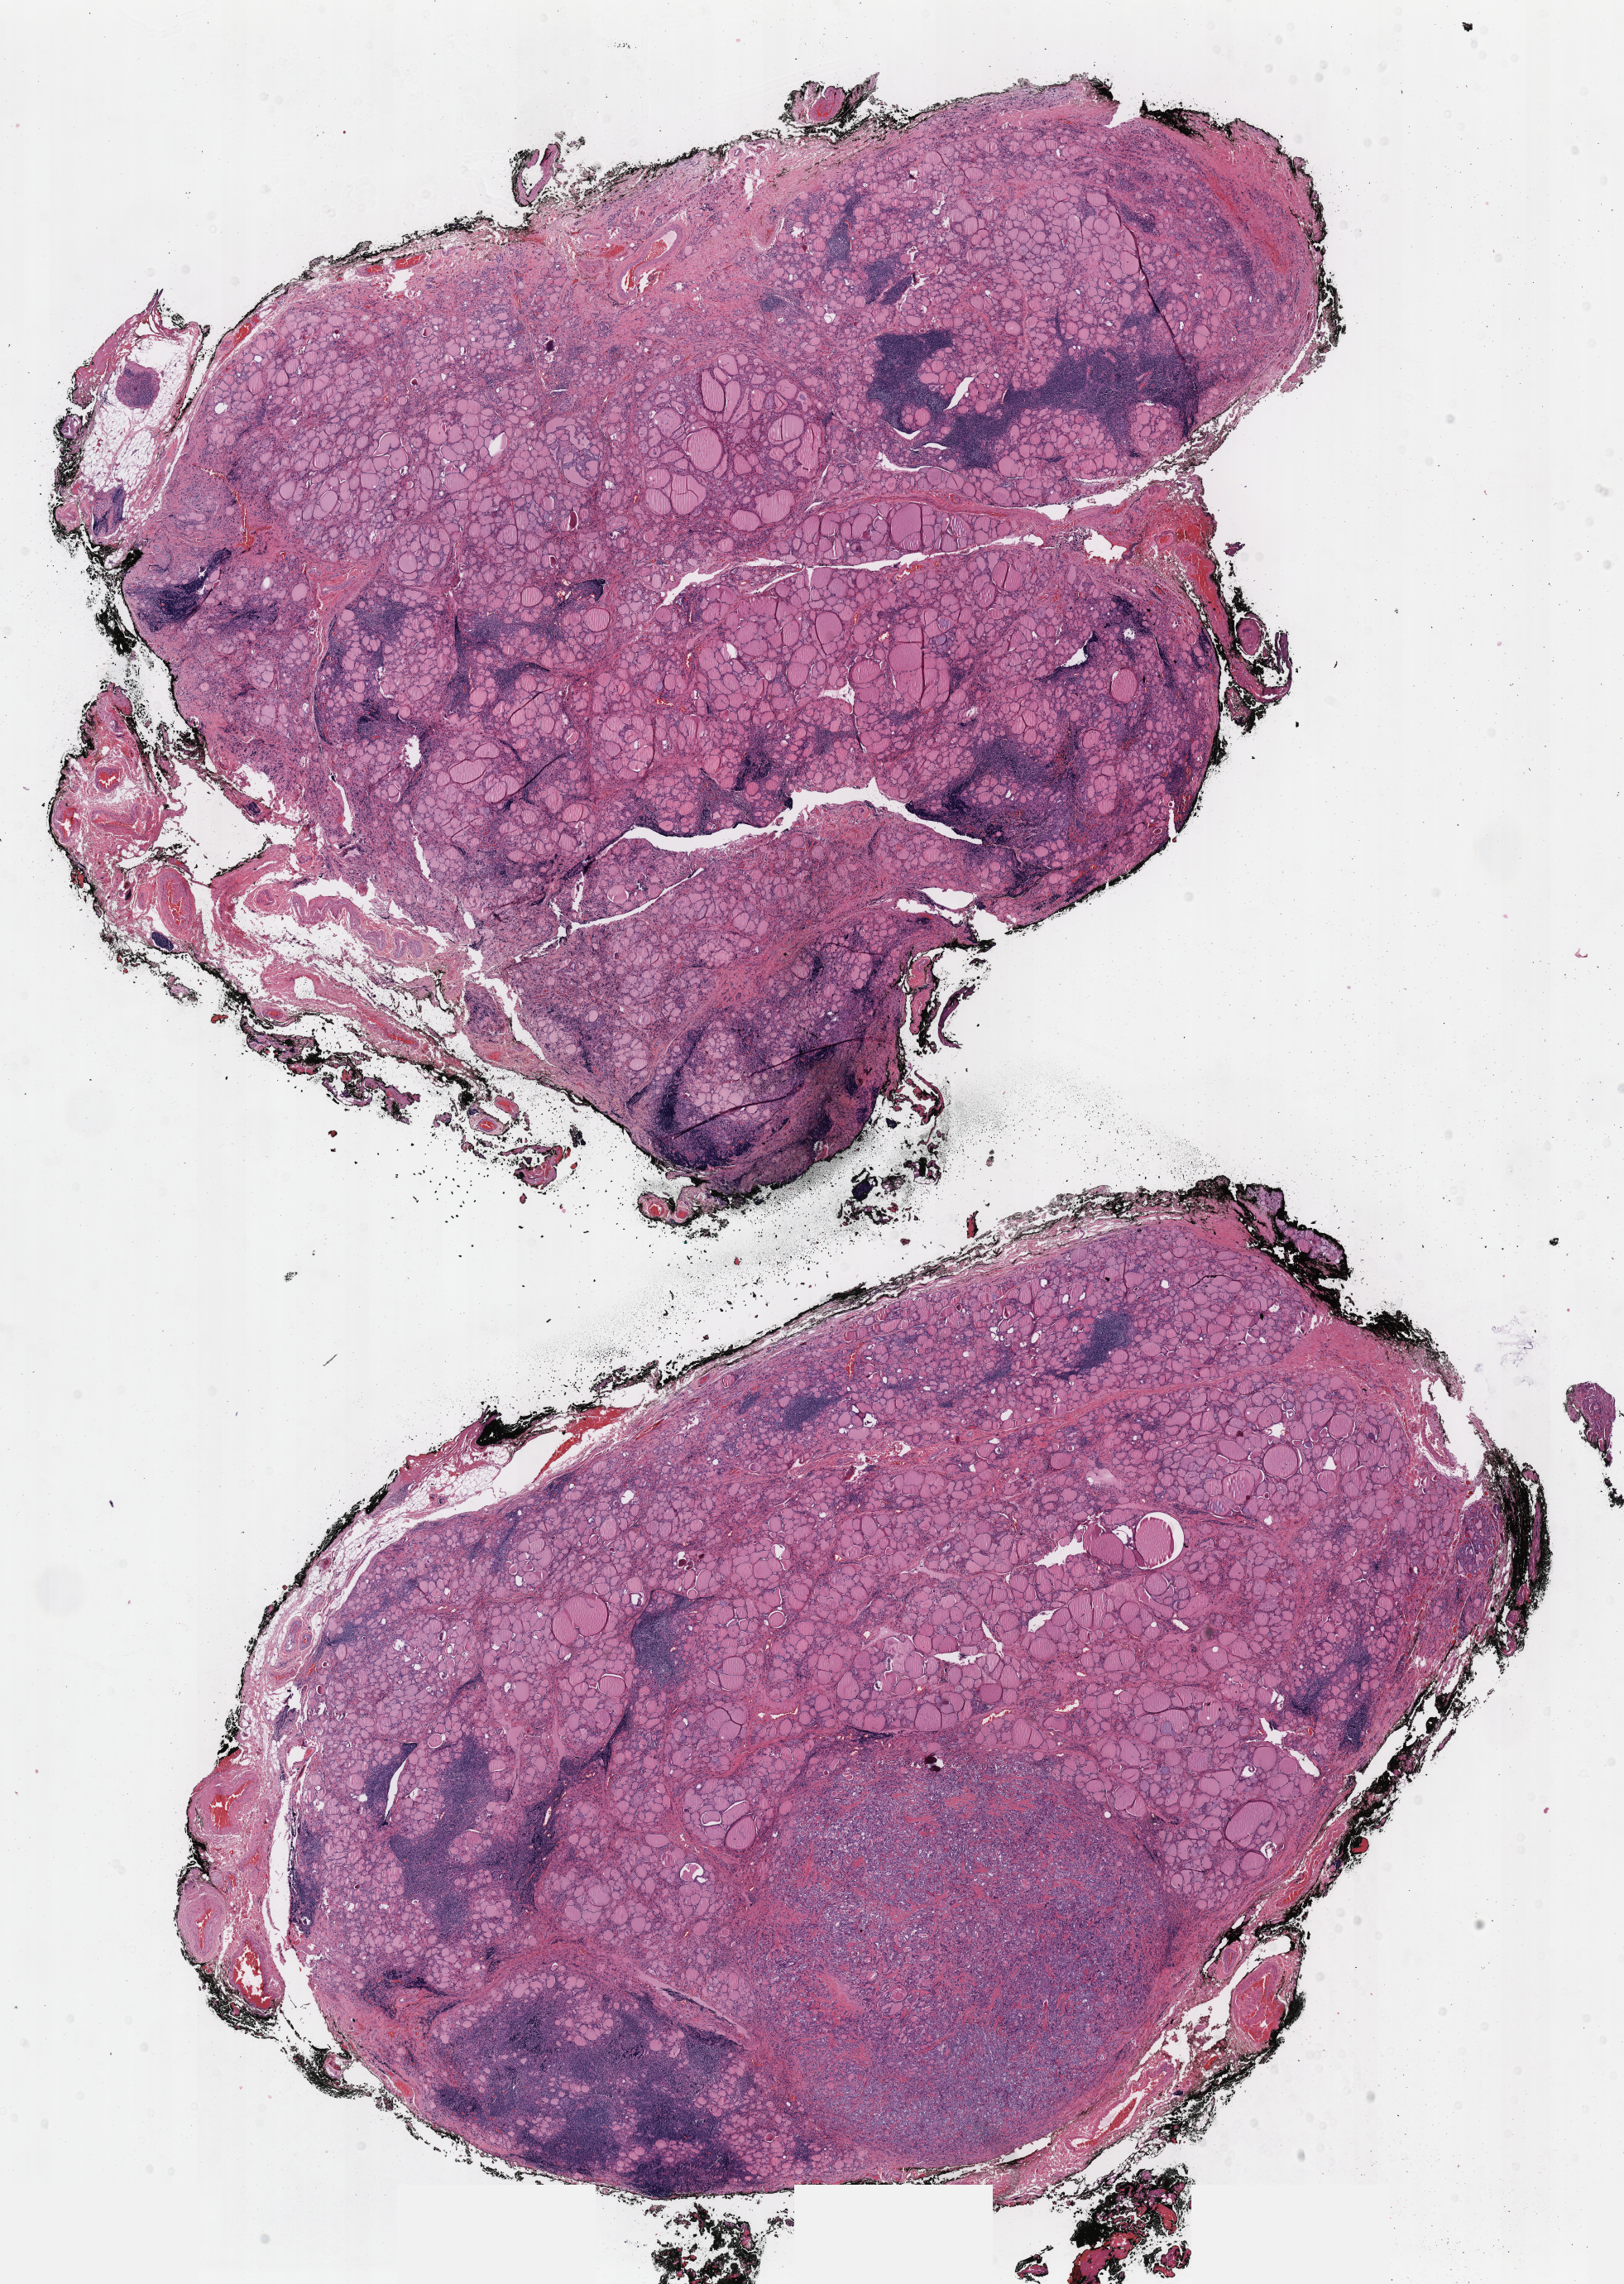
Whole-slide histology image, Hematoxylin and eosin (H&E) stained — a low-resolution overview of the entire scanned area, about 15.5 x 21.7 mm (slide scanned at 40x), formalin-fixed paraffin-embedded (FFPE) diagnostic section, thyroid, primary tumour sample. Female, age 55 years at initial diagnosis.
TNM: T1a N0 MX. Diagnosis: Papillary carcinoma, follicular variant (thyroid gland). Laterality: bilateral. AJCC pathologic stage: I.